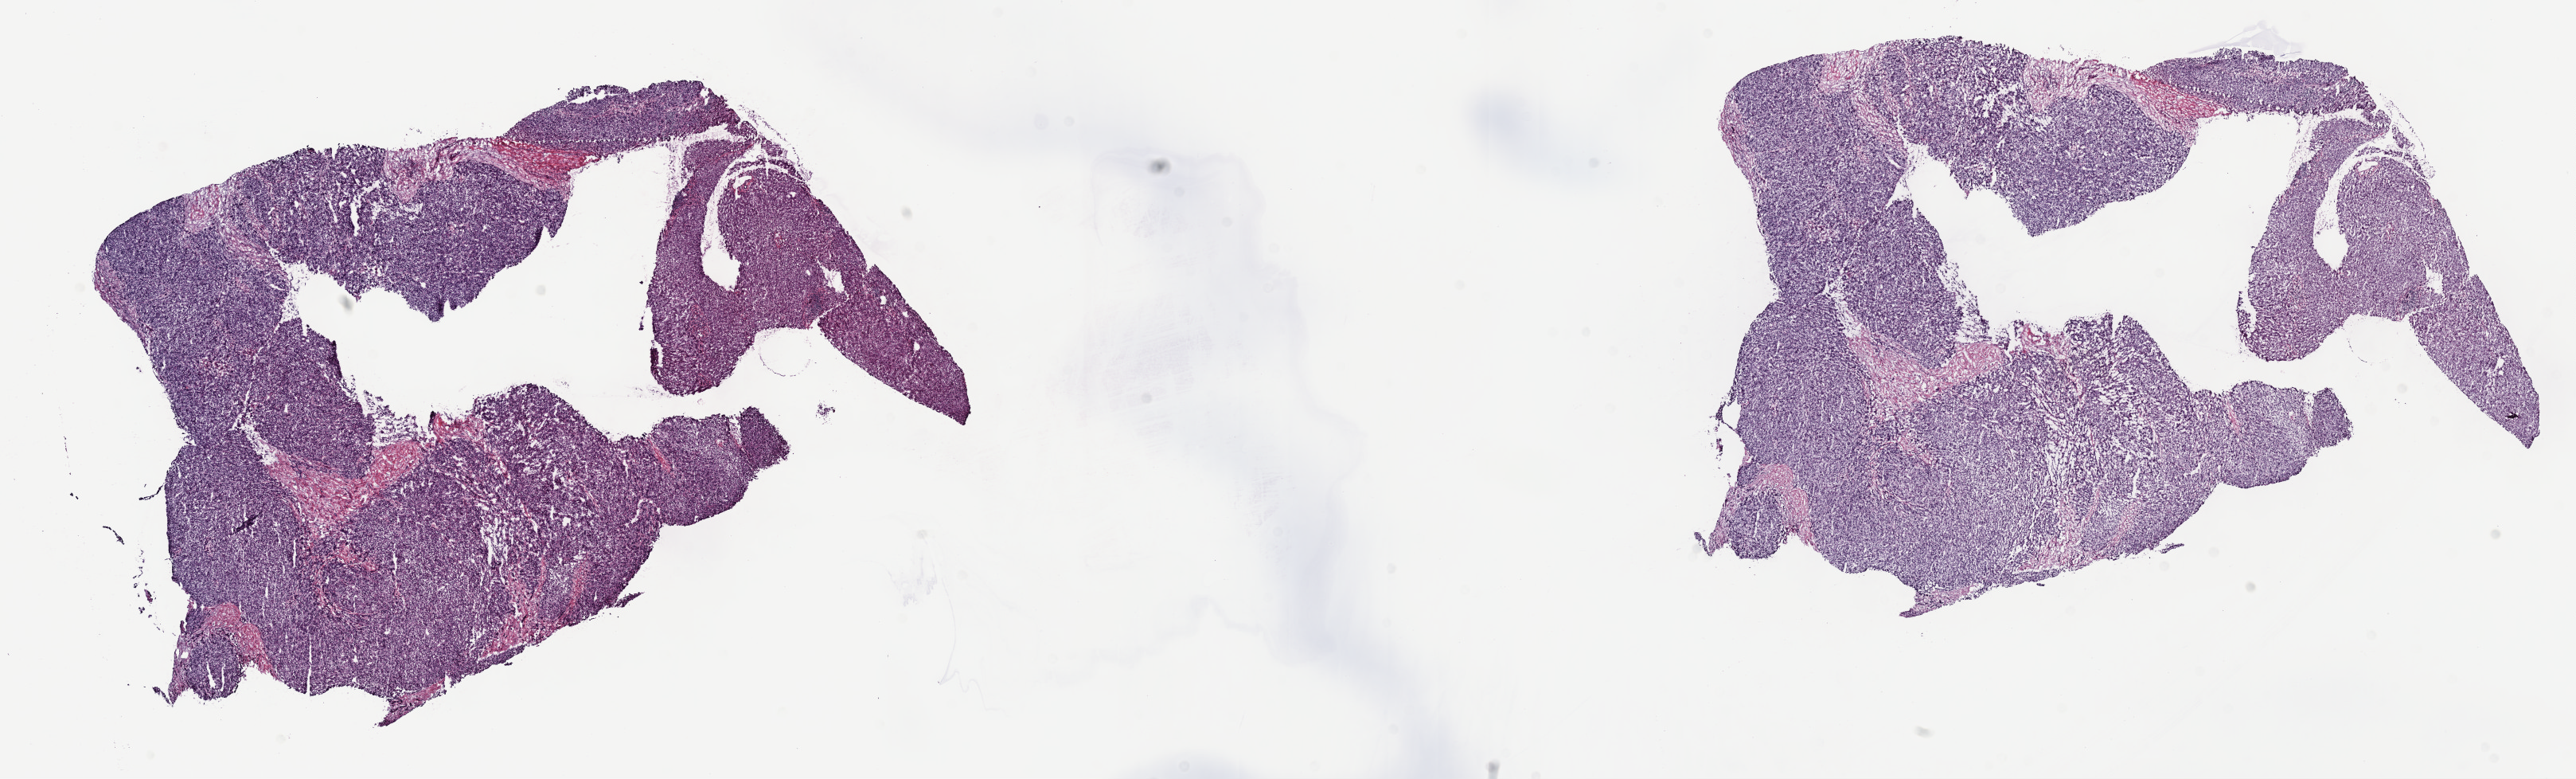
H&E whole-slide image, low-resolution overview of the scanned area, about 26.2 x 7.9 mm (slide scanned at 40x). Frozen section. Liver, primary tumour sample. Male patient; age at initial diagnosis 32 years. Histologic grade: G3 (poorly differentiated). Composition of this section per pathologist review: tumour cells 70%, tumour nuclei 70%, normal cells 15%, stromal cells 15%, necrosis 0%. Inflammatory infiltration, as recorded: lymphocyte infiltration 4%, monocyte infiltration 1%, neutrophil infiltration 1%.
AJCC pathologic stage: I. Histologic diagnosis: Hepatocellular carcinoma, NOS.